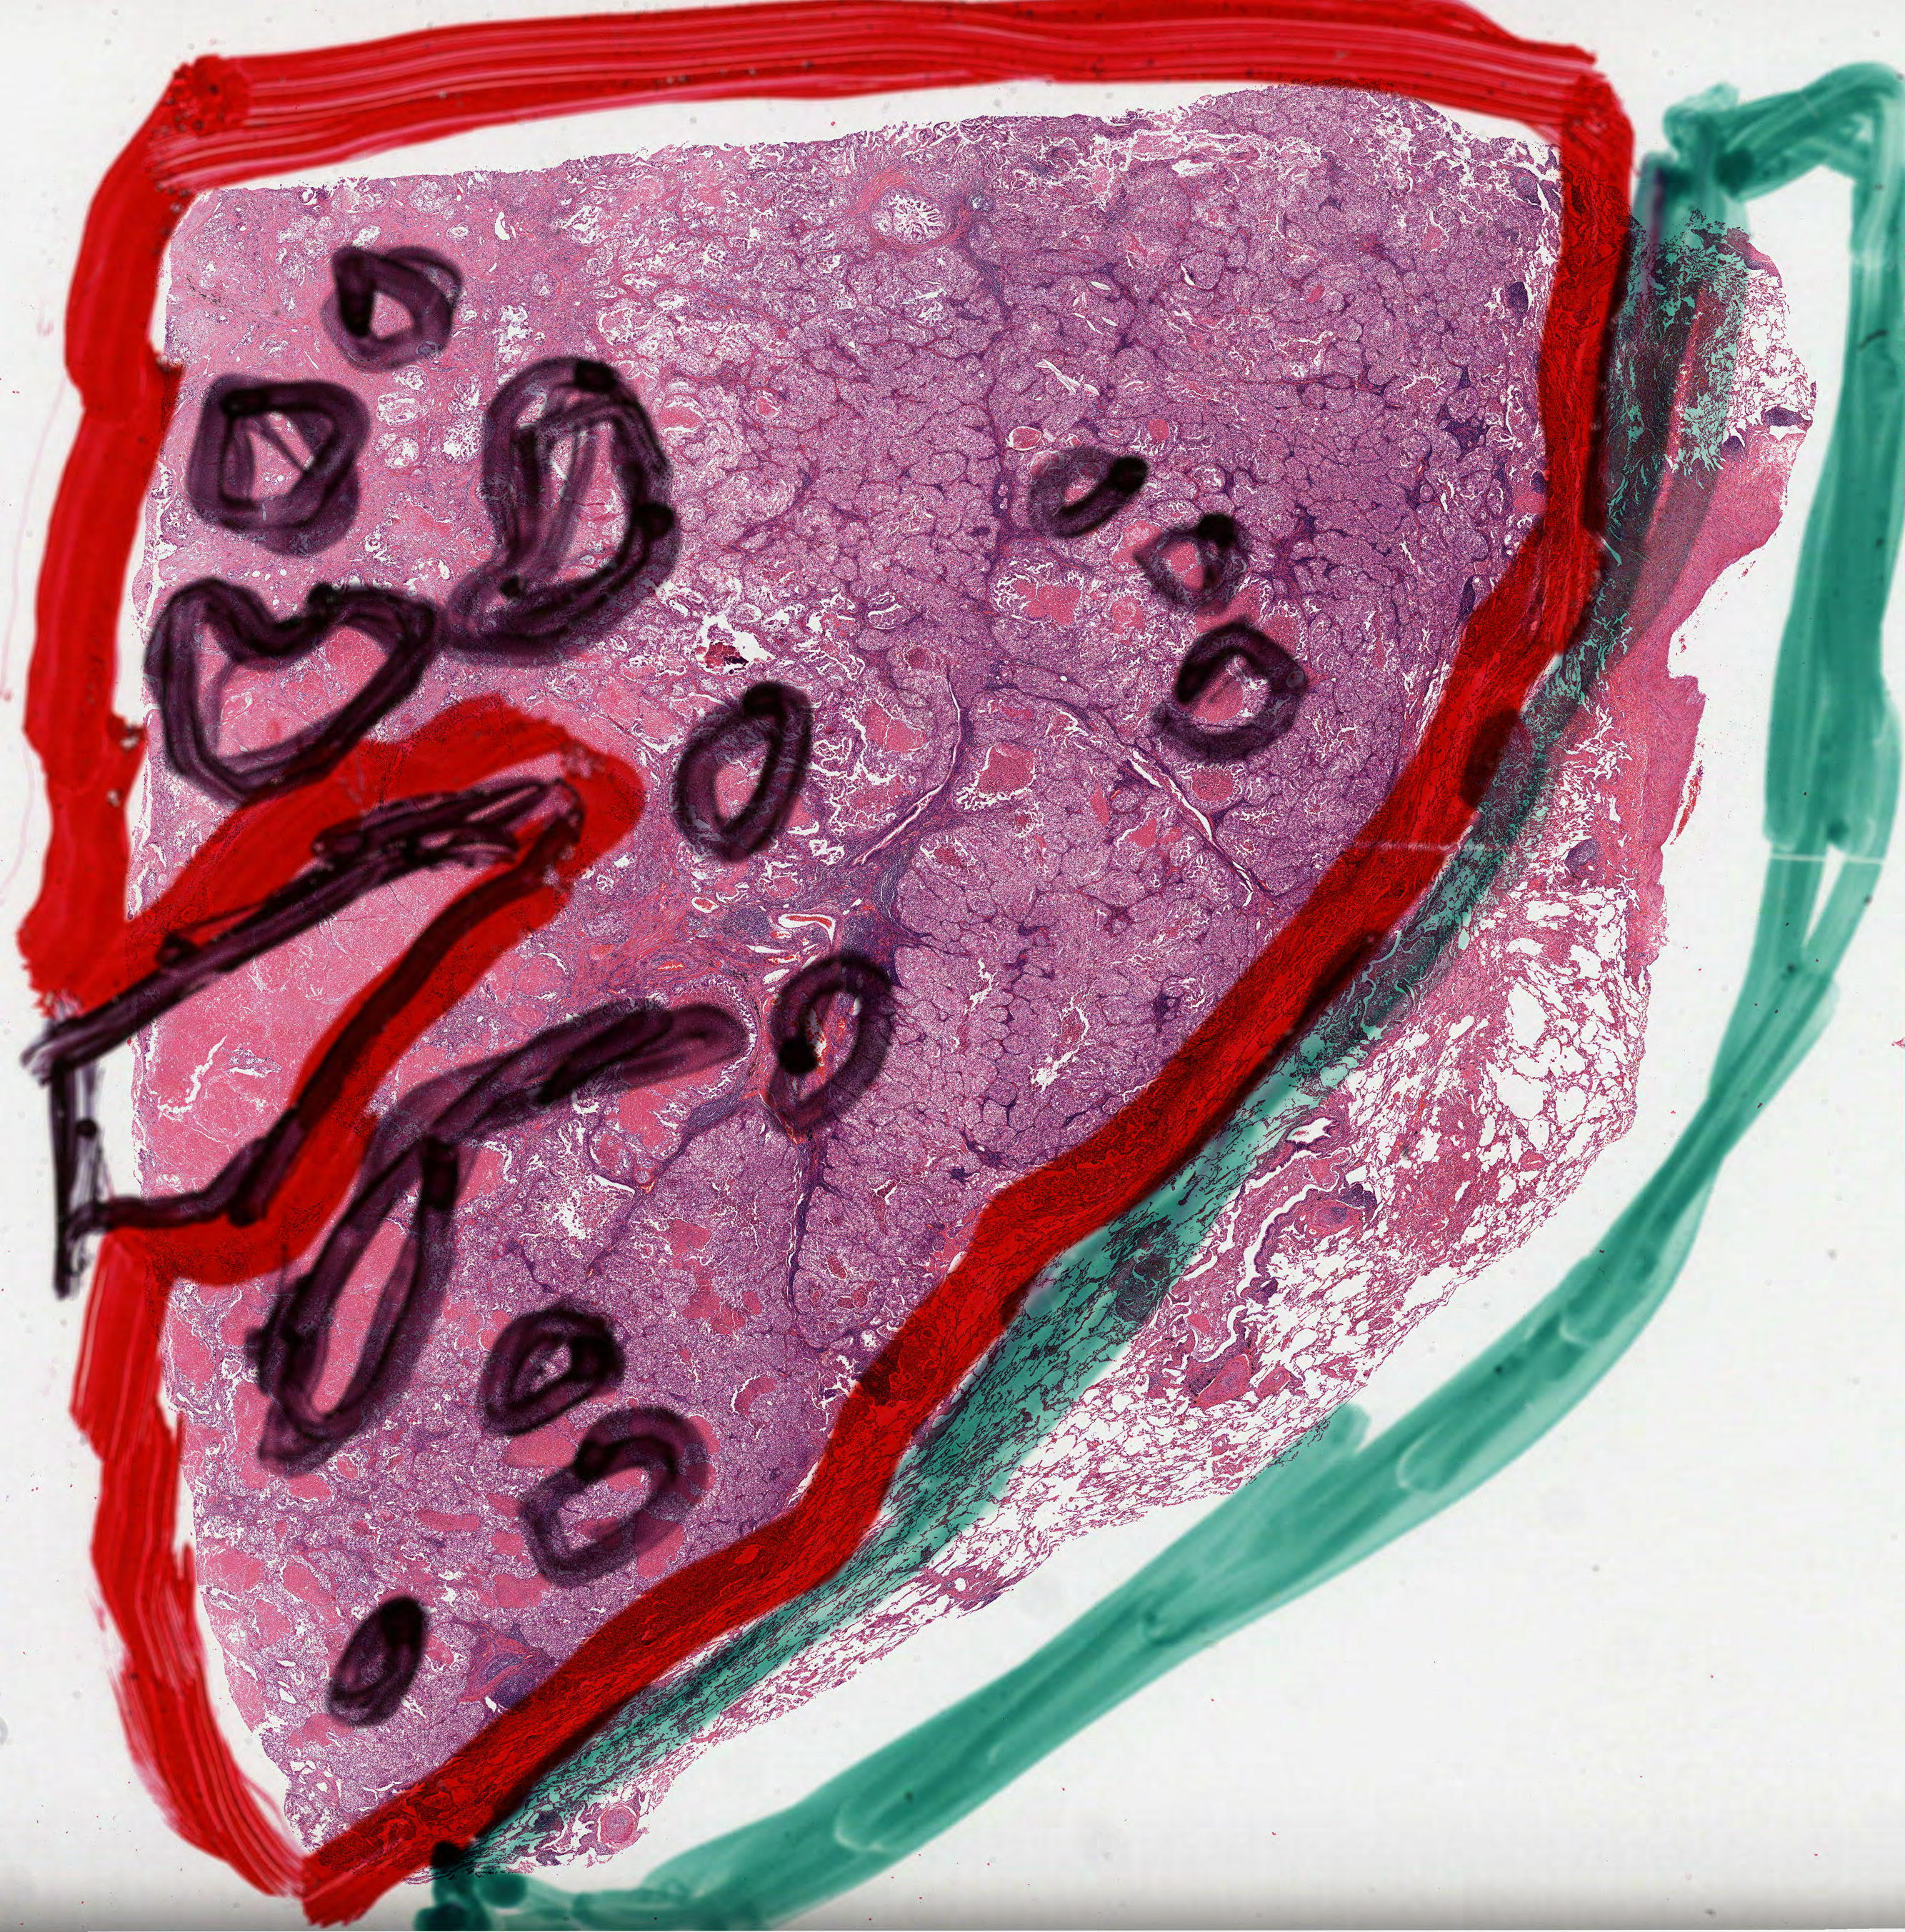
Whole-slide histology image, H&E-stained, shown as a low-resolution overview of the whole scanned area (about 21.5 x 21.8 mm), FFPE section, primary tumour sample from the lung. Male patient; age at initial diagnosis 62 years.
AJCC pathologic stage: IB (7th edition). Histologic diagnosis: Adenocarcinoma, NOS (lower lobe, lung).